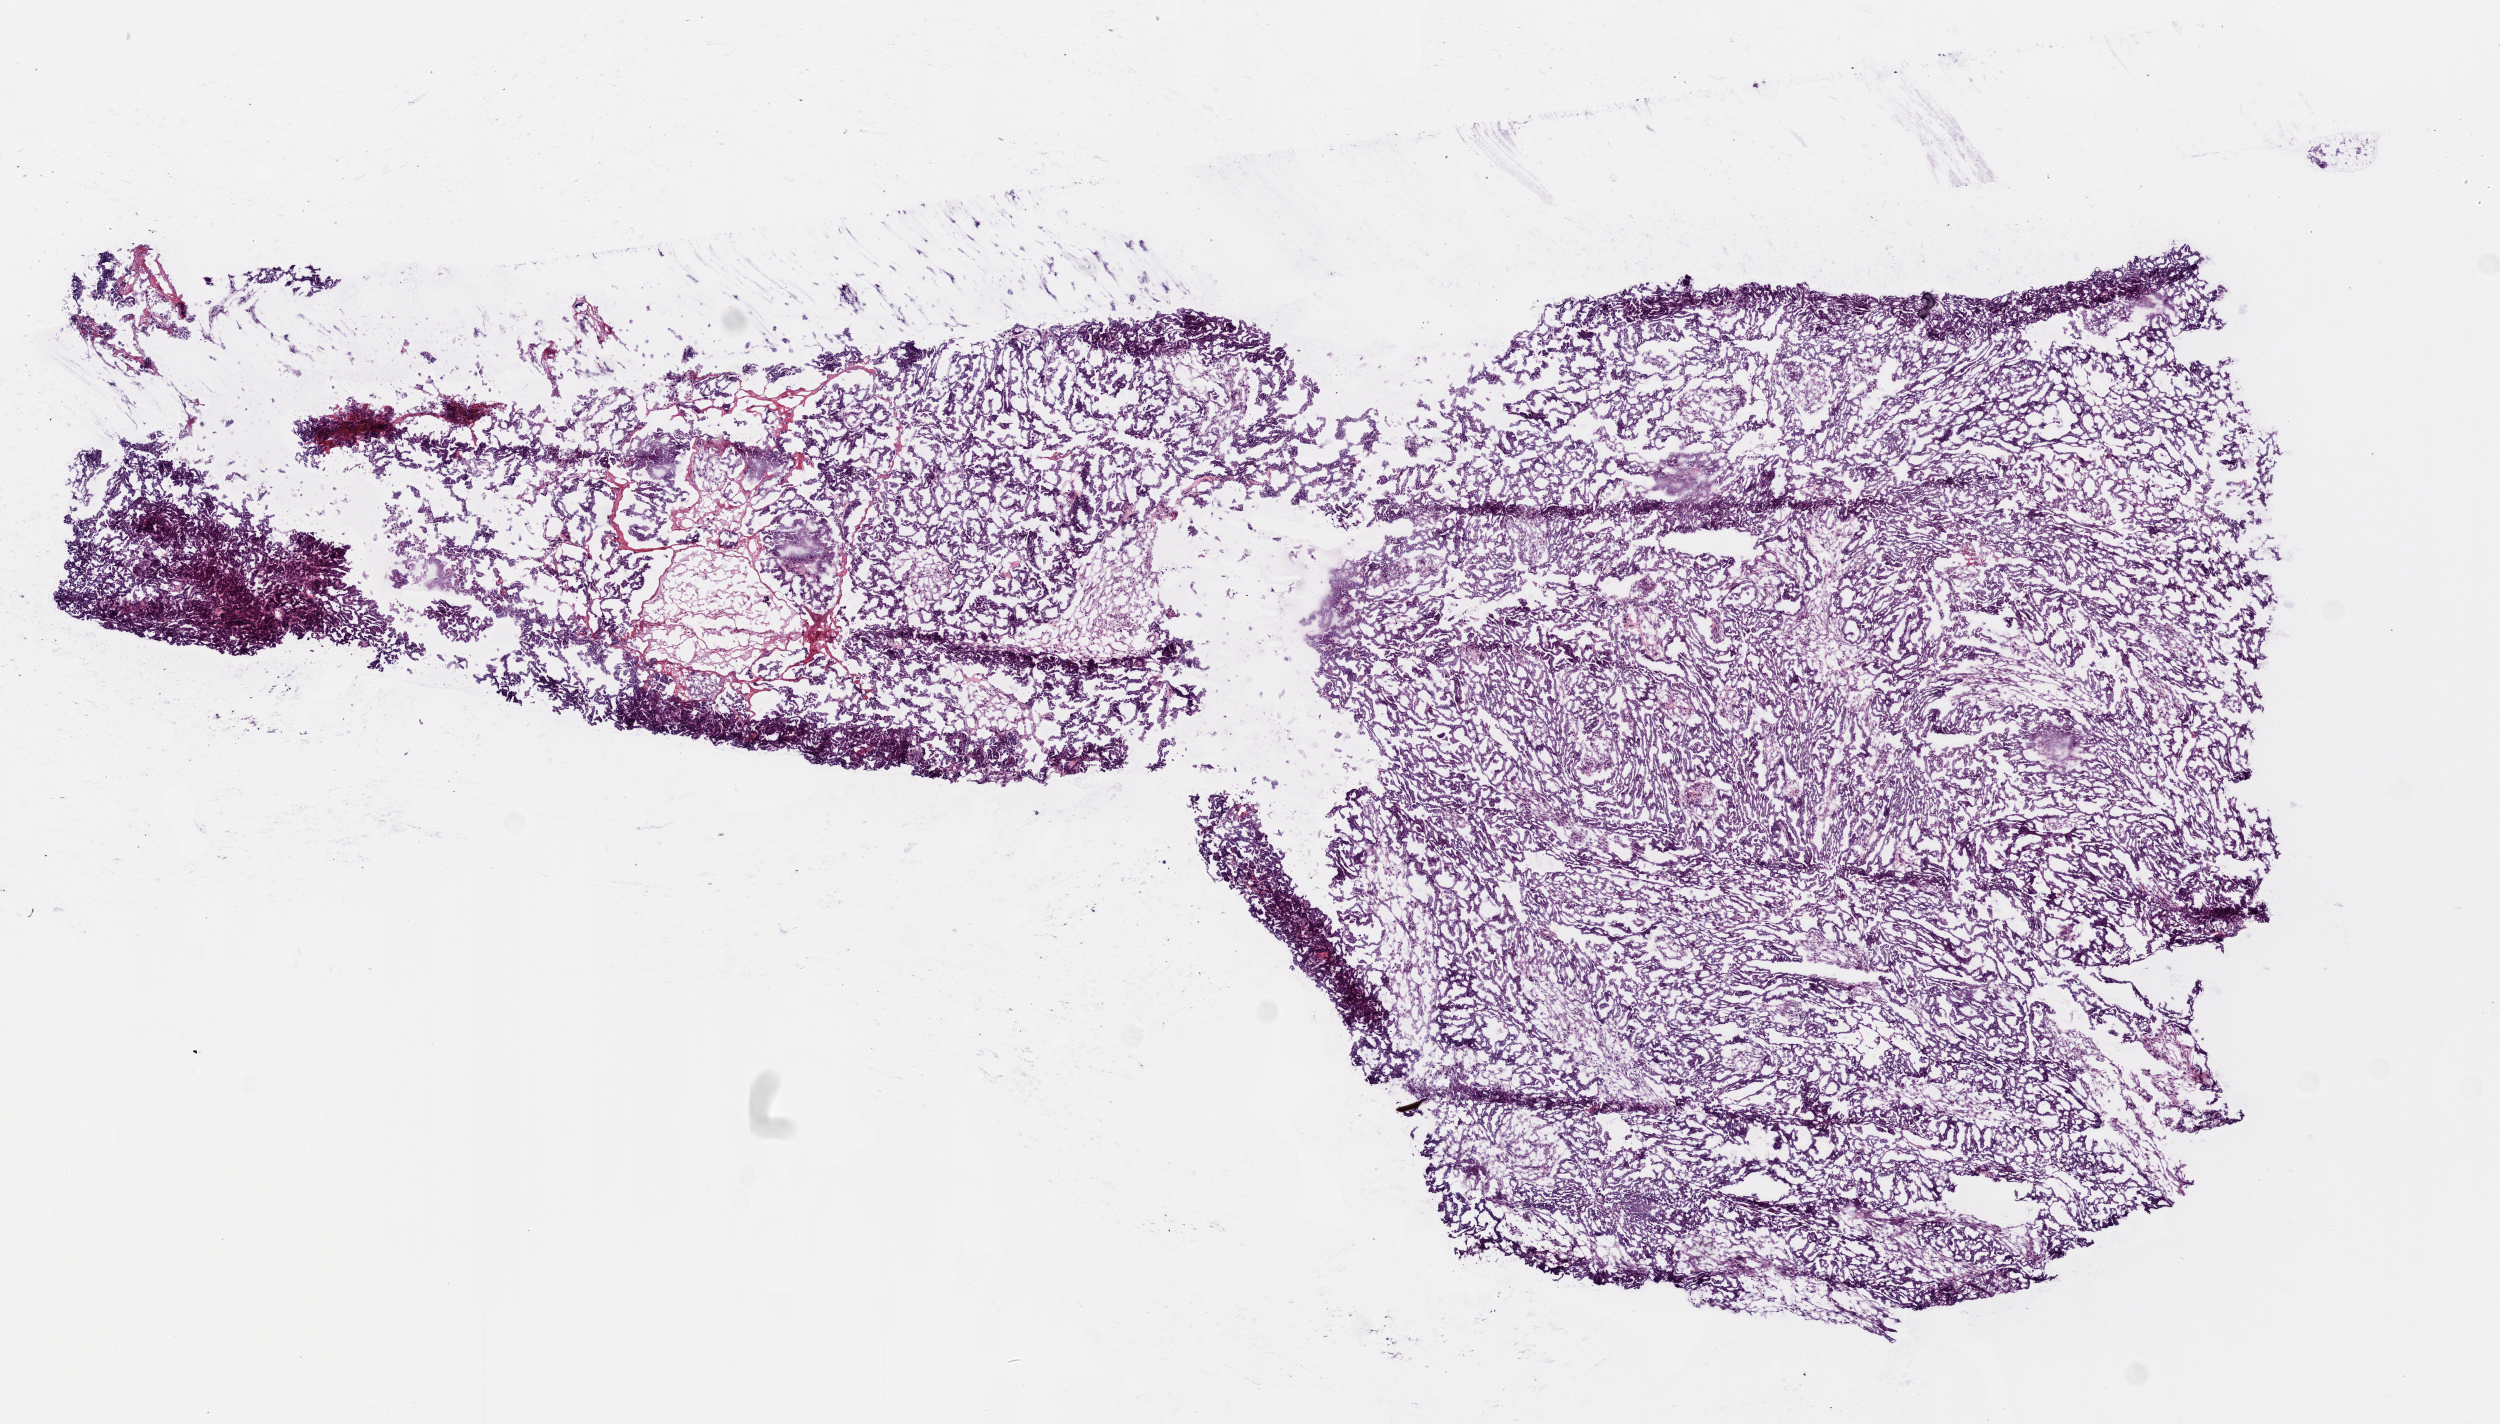
Digitized Hematoxylin and eosin (H&E) stained tissue section (whole slide) — whole scanned area (about 10.0 x 5.7 mm) shown as a low-resolution overview, frozen section from the top of the tissue portion, primary tumour sample from the ovary. Female, age 49 years at initial diagnosis. Histologic grade: G3 (poorly differentiated). Pathologist review of this section (percent, as recorded): tumour cells 90%, tumour nuclei 90%, normal cells 0%, stromal cells 10%, necrosis 0%.
Pathologic diagnosis: Serous cystadenocarcinoma, NOS. Laterality: bilateral. FIGO stage: IV.